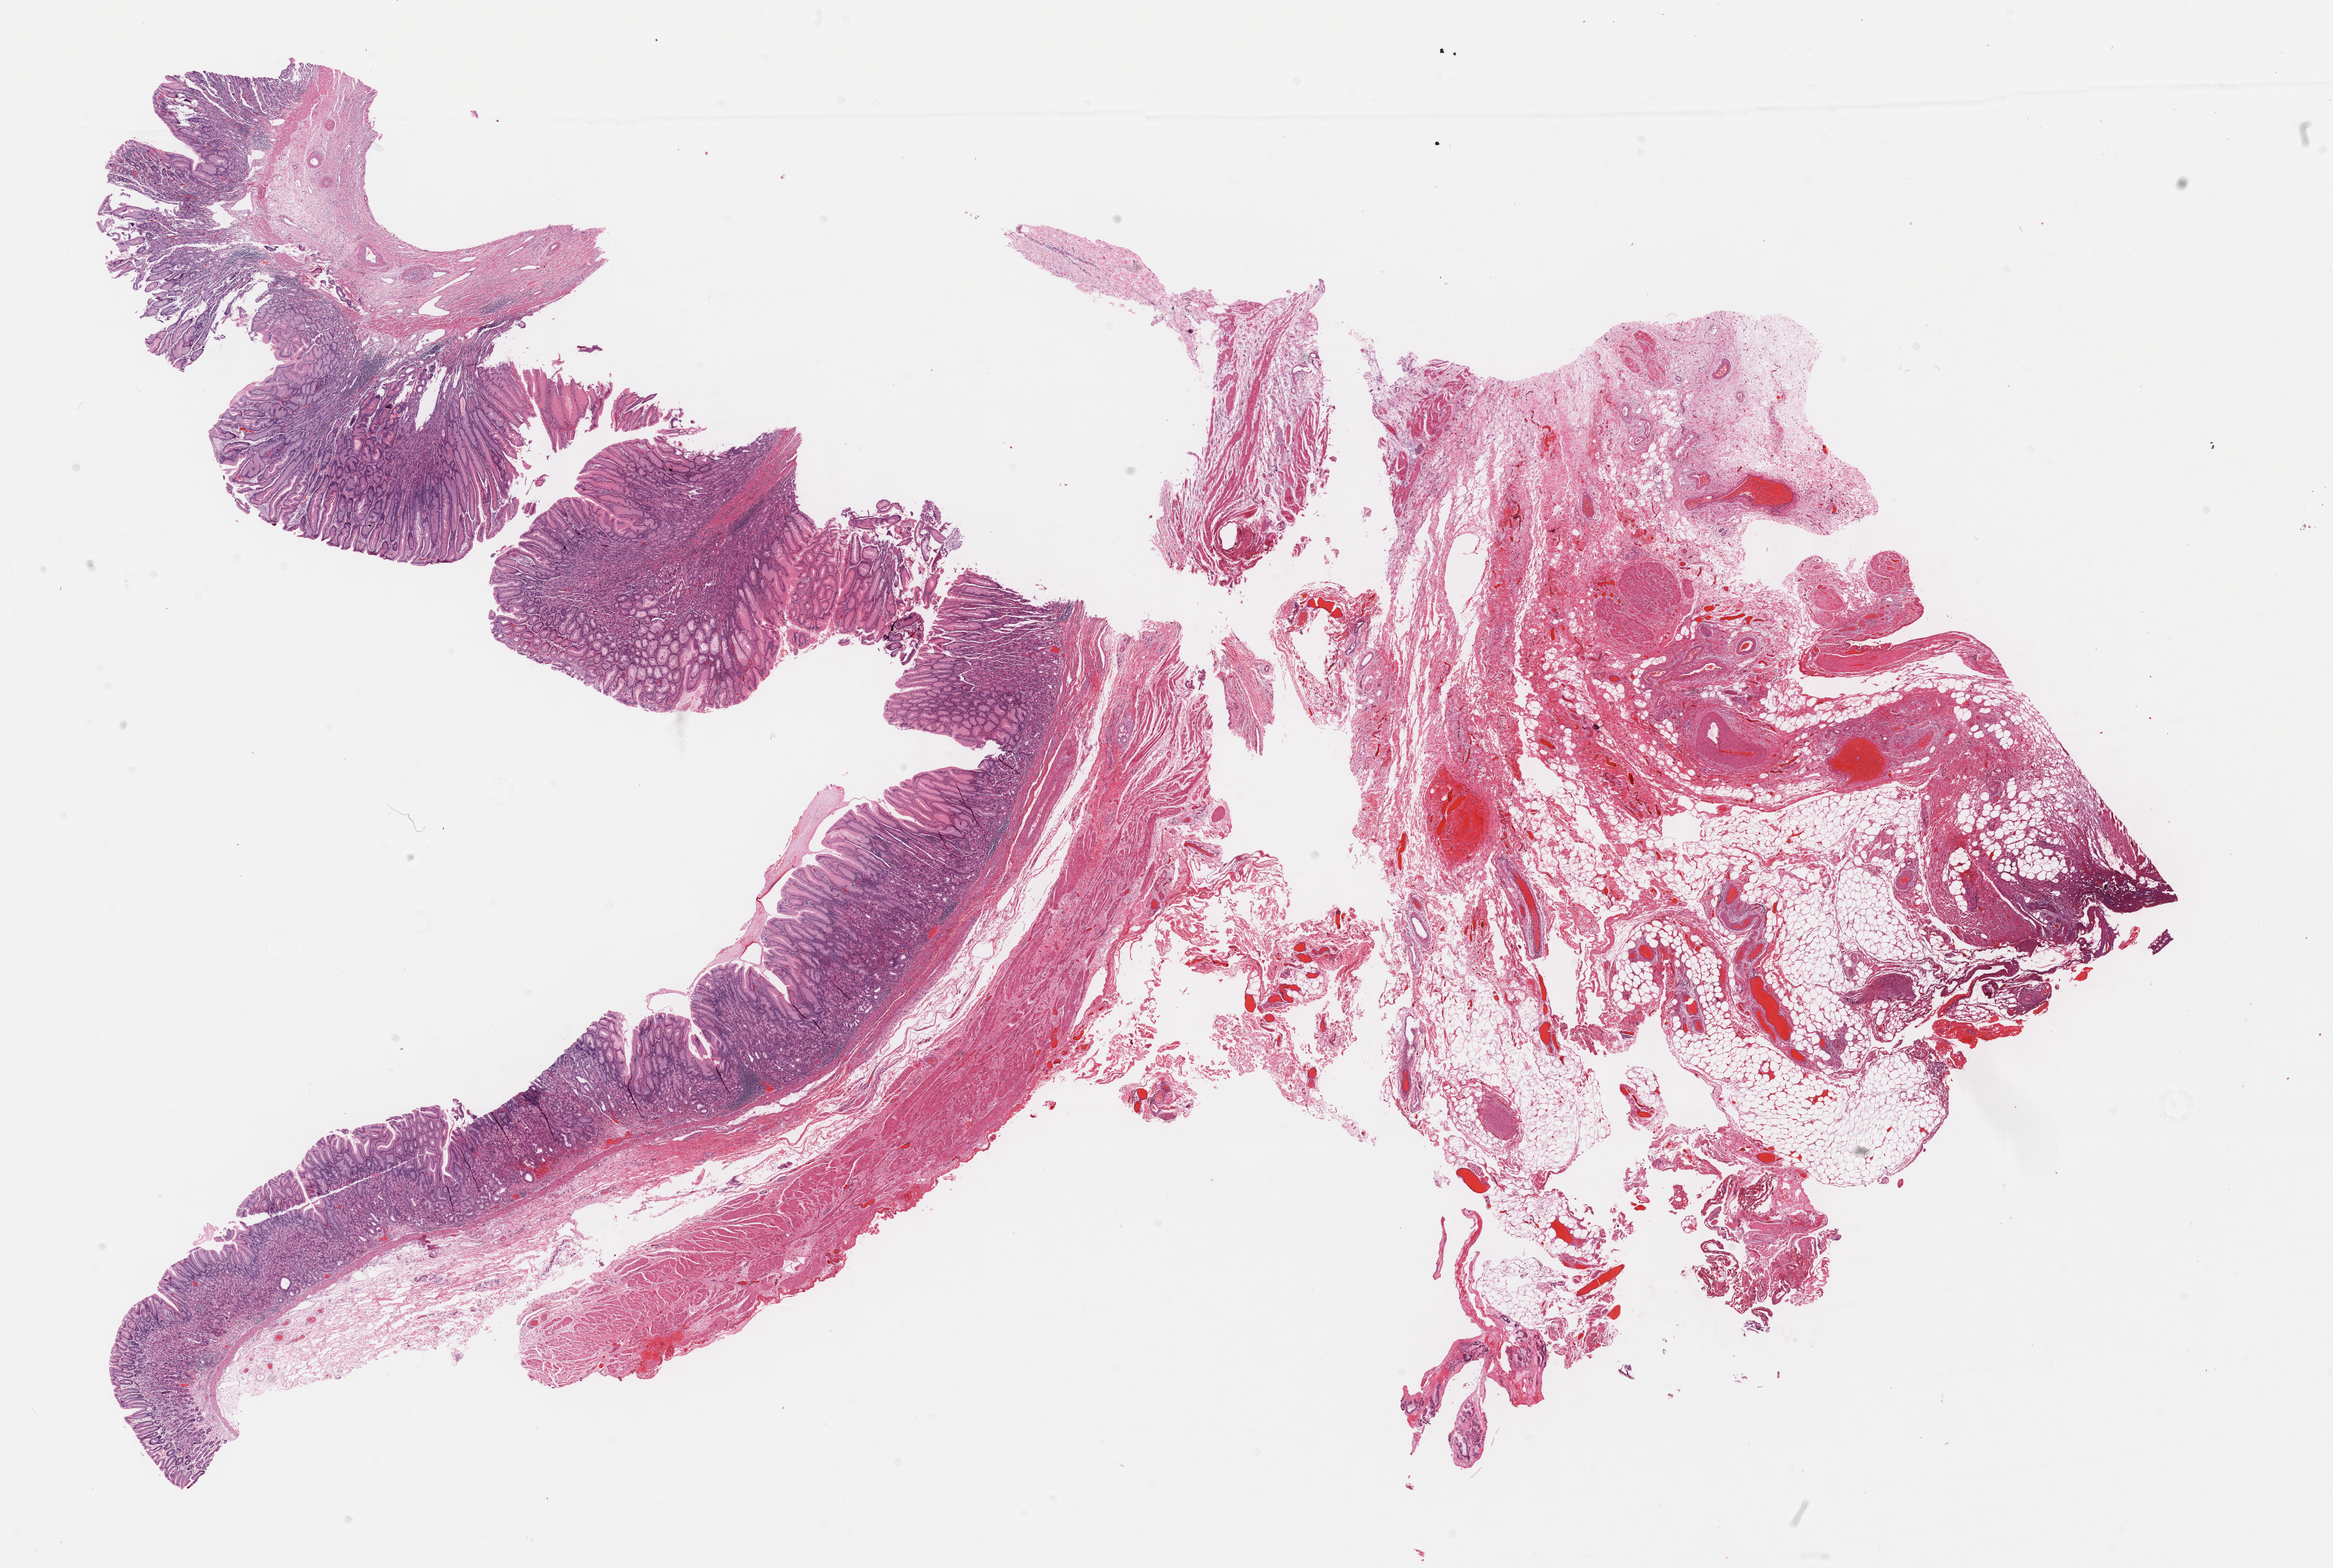
H&E-stained whole-slide image — shown as a low-resolution overview of the whole scanned area (about 28.7 x 19.3 mm, acquisition: 40x scan). FFPE section. Sample: primary tumour, stomach. Patient: female, age at initial diagnosis 58 years.
Pathologic diagnosis: Leiomyosarcoma, NOS.